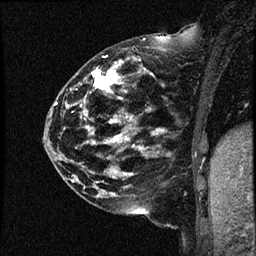
Breast MRI (dynamic contrast-enhanced), one sagittal slice. Position 17 of 44 along the scan axis. Dynamic contrast-enhanced study with each time point stored as its own series, time point 2 of 4 at this slice position (early post-contrast, ordered by acquisition time). 1.5 T. TE 4.2 ms, TR 17.7 ms. 256 × 256 image matrix, field of view 200 × 200 mm. Patient: female, 52 years. From the clinical record (not read from this slice): setting: breast cancer imaged before/during neoadjuvant chemotherapy; receptor status: HR-positive, HER2-negative.
Annotated regions visible in this slice (semi-automatic segmentation, software-assisted and operator-edited):
- analysis volume of interest (the breast-tissue region the enhancement analysis was run in; not a lesion): box from (x=47, y=48) to (x=163, y=147) px
- tumour enhancement mask (voxels above the 100 % enhancement threshold inside the analysis volume of interest): (x=85, y=57)–(x=159, y=143)